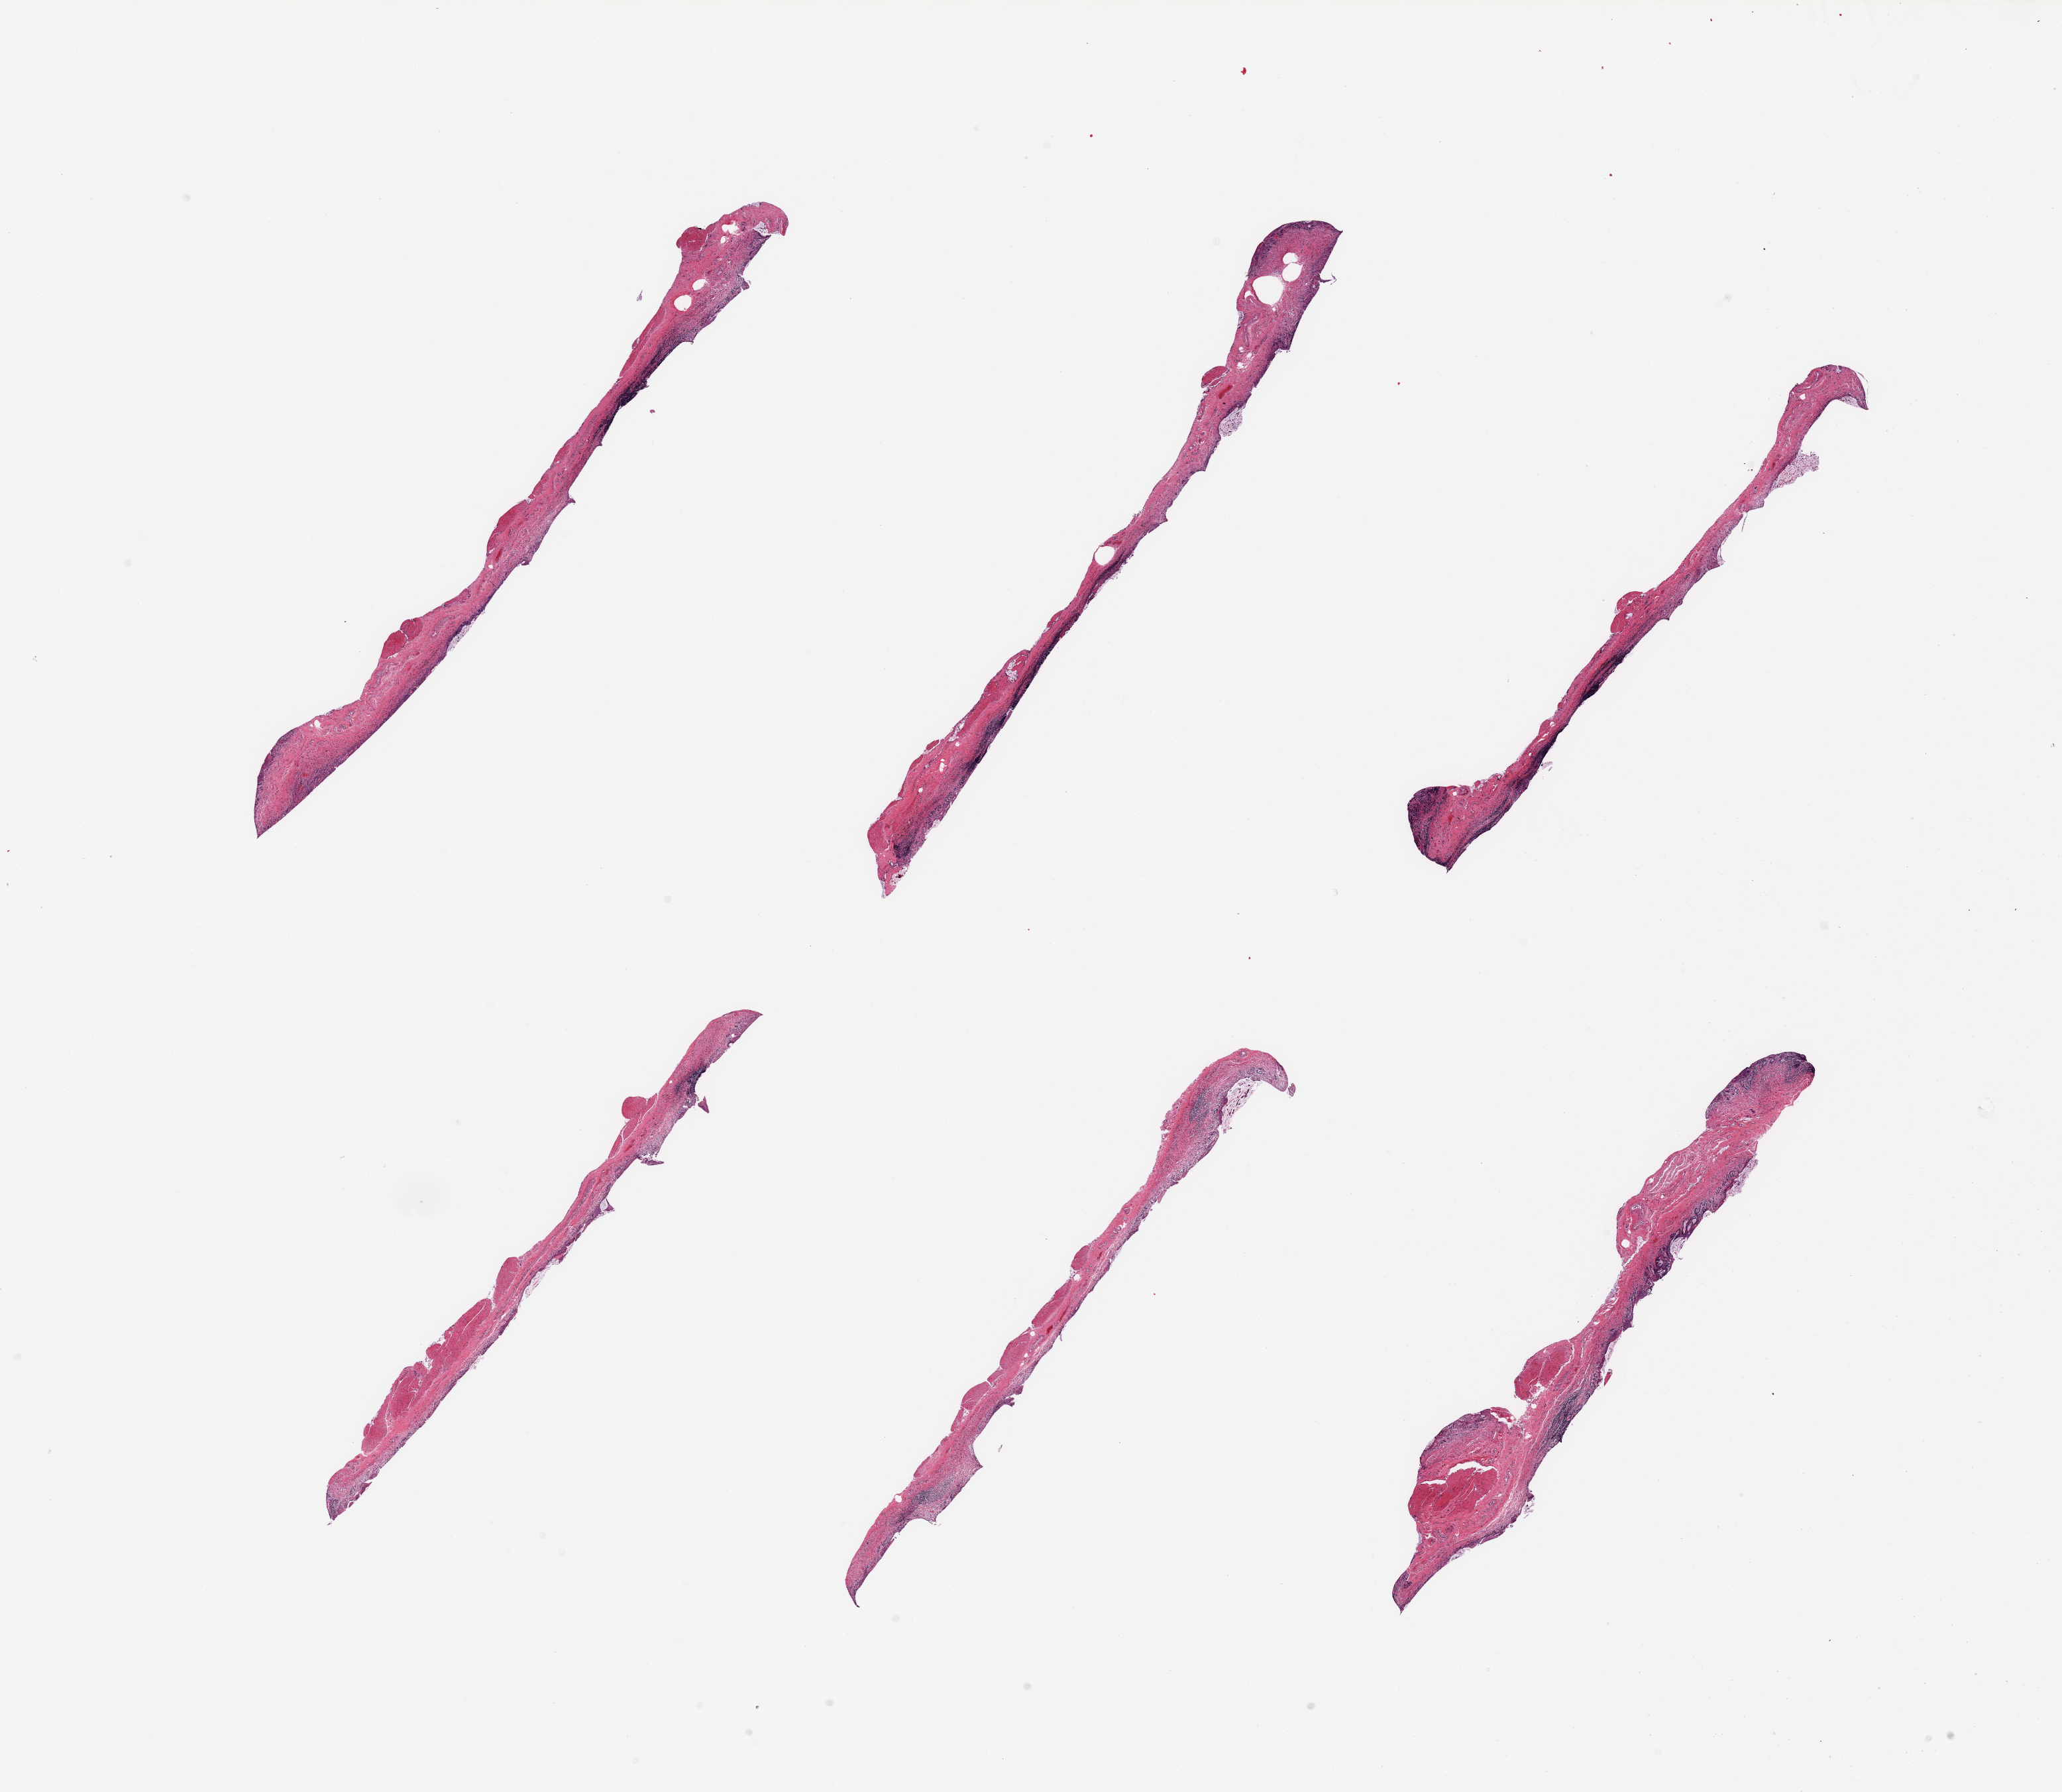
Digitized hematoxylin and eosin (H&E)-stained section, low-resolution overview of the scanned area, about 24.6 x 21.4 mm (from a 20x scan). PAXgene-fixed, paraffin-embedded tissue. Section of ileum (target tissue). Tissue donor sample. Donor sex: female.
Reviewer comment on this tissue sample: 6 pieces; insufficient lymphoid tissue.